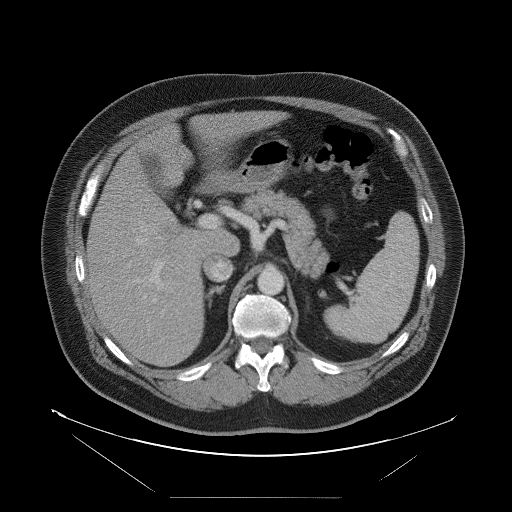
Contrast-enhanced abdominal CT, one axial slice; slice 57 of 114 in the series (ordered by position); soft-tissue window (W 400 / L 40 HU); 5 mm slice thickness; 512 × 512 image matrix, field of view 500 × 500 mm. Male patient, age 61 years. Case-level facts recorded for this patient, not image findings: diagnosis: colorectal cancer liver metastases, imaged before liver resection; multiple liver metastases: no.
Structures marked on this image (outlined manually by an expert reader):
- hepatic veins: box from (x=136, y=231) to (x=147, y=245) px
- liver: (x=88, y=112)–(x=276, y=366)
- planned liver remnant (the part of the liver to remain after resection): (x=145, y=112)–(x=278, y=182)
- portal vein (with intrahepatic branches): (x=140, y=215)–(x=211, y=302)
- liver metastasis: (x=163, y=226)–(x=178, y=238)